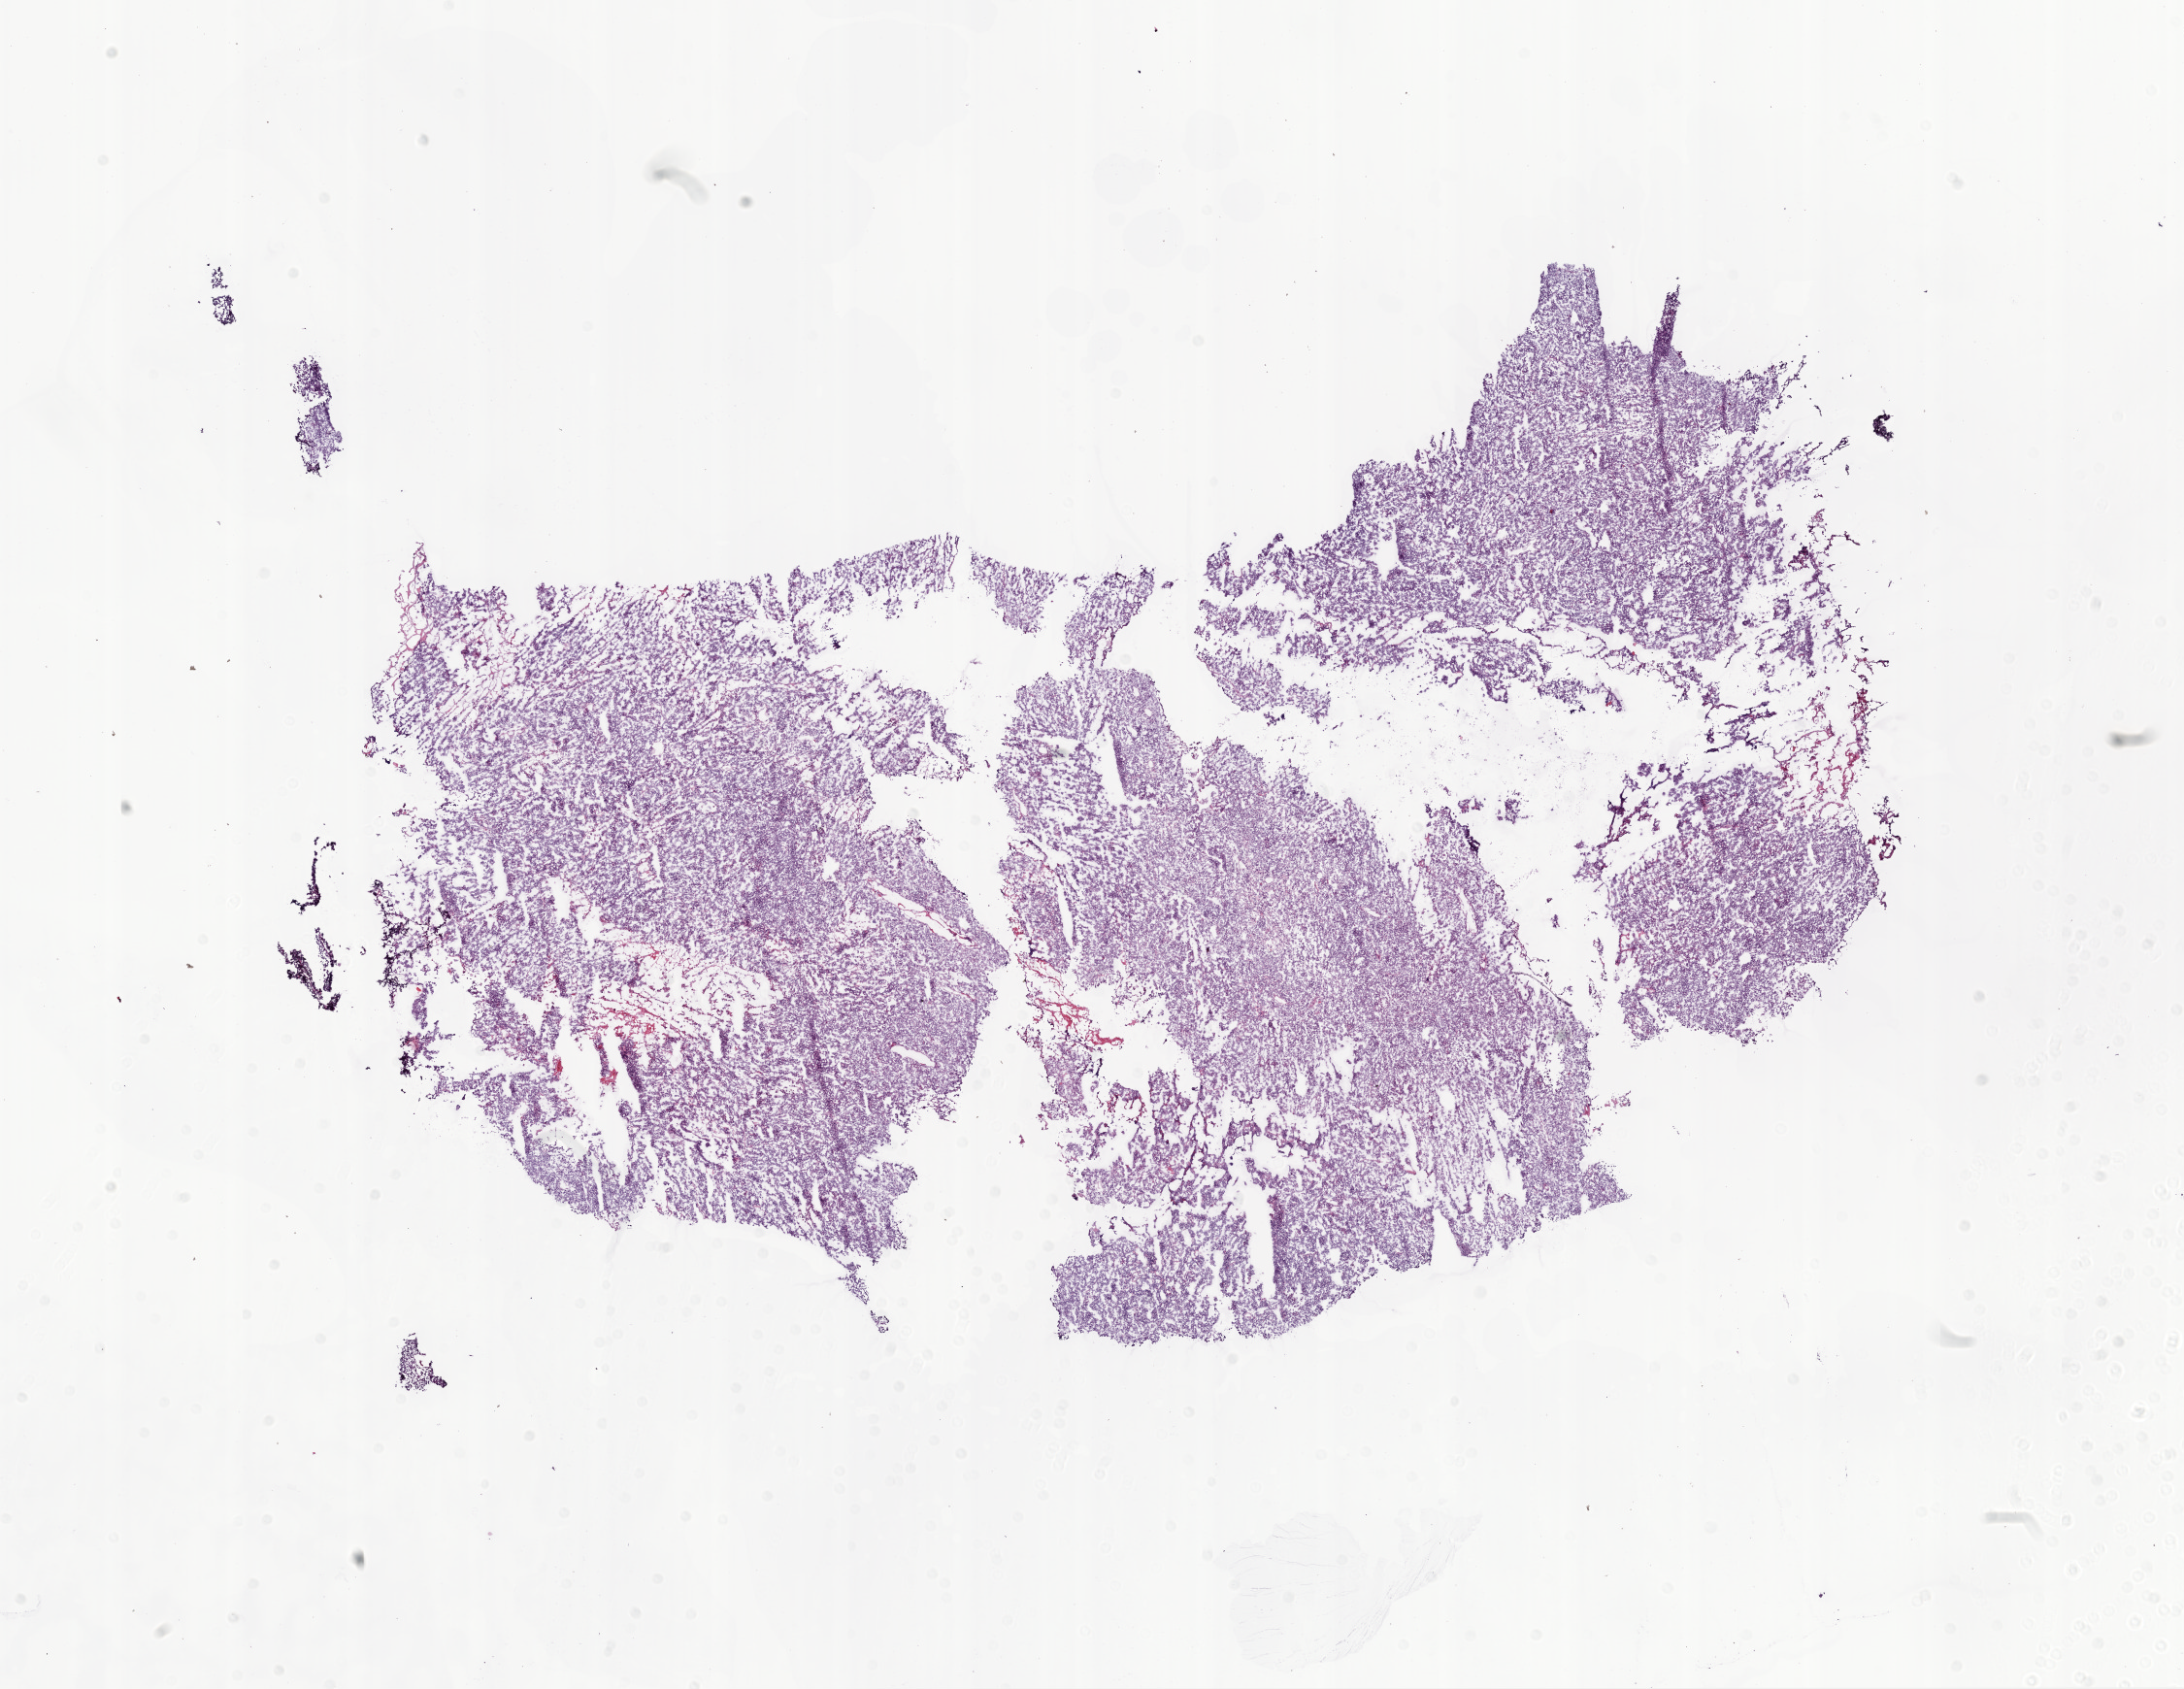
Hematoxylin and eosin (H&E) stained whole-slide image — low-resolution overview of the scanned area, about 18.1 x 14.0 mm (from a 20x scan), frozen section, ovary, primary tumour sample. Patient: female, age at initial diagnosis 81 years. Histologic grade: G3 (poorly differentiated). Pathologist review of this section (percent, as recorded): tumour cells 90%, tumour nuclei 90%, normal cells 0%, stromal cells 10%, necrosis 0%. Inflammatory infiltration, as recorded: lymphocyte infiltration 0%, monocyte infiltration 0%, neutrophil infiltration 0%.
FIGO stage: IIIC. Diagnosis: Serous cystadenocarcinoma, NOS.